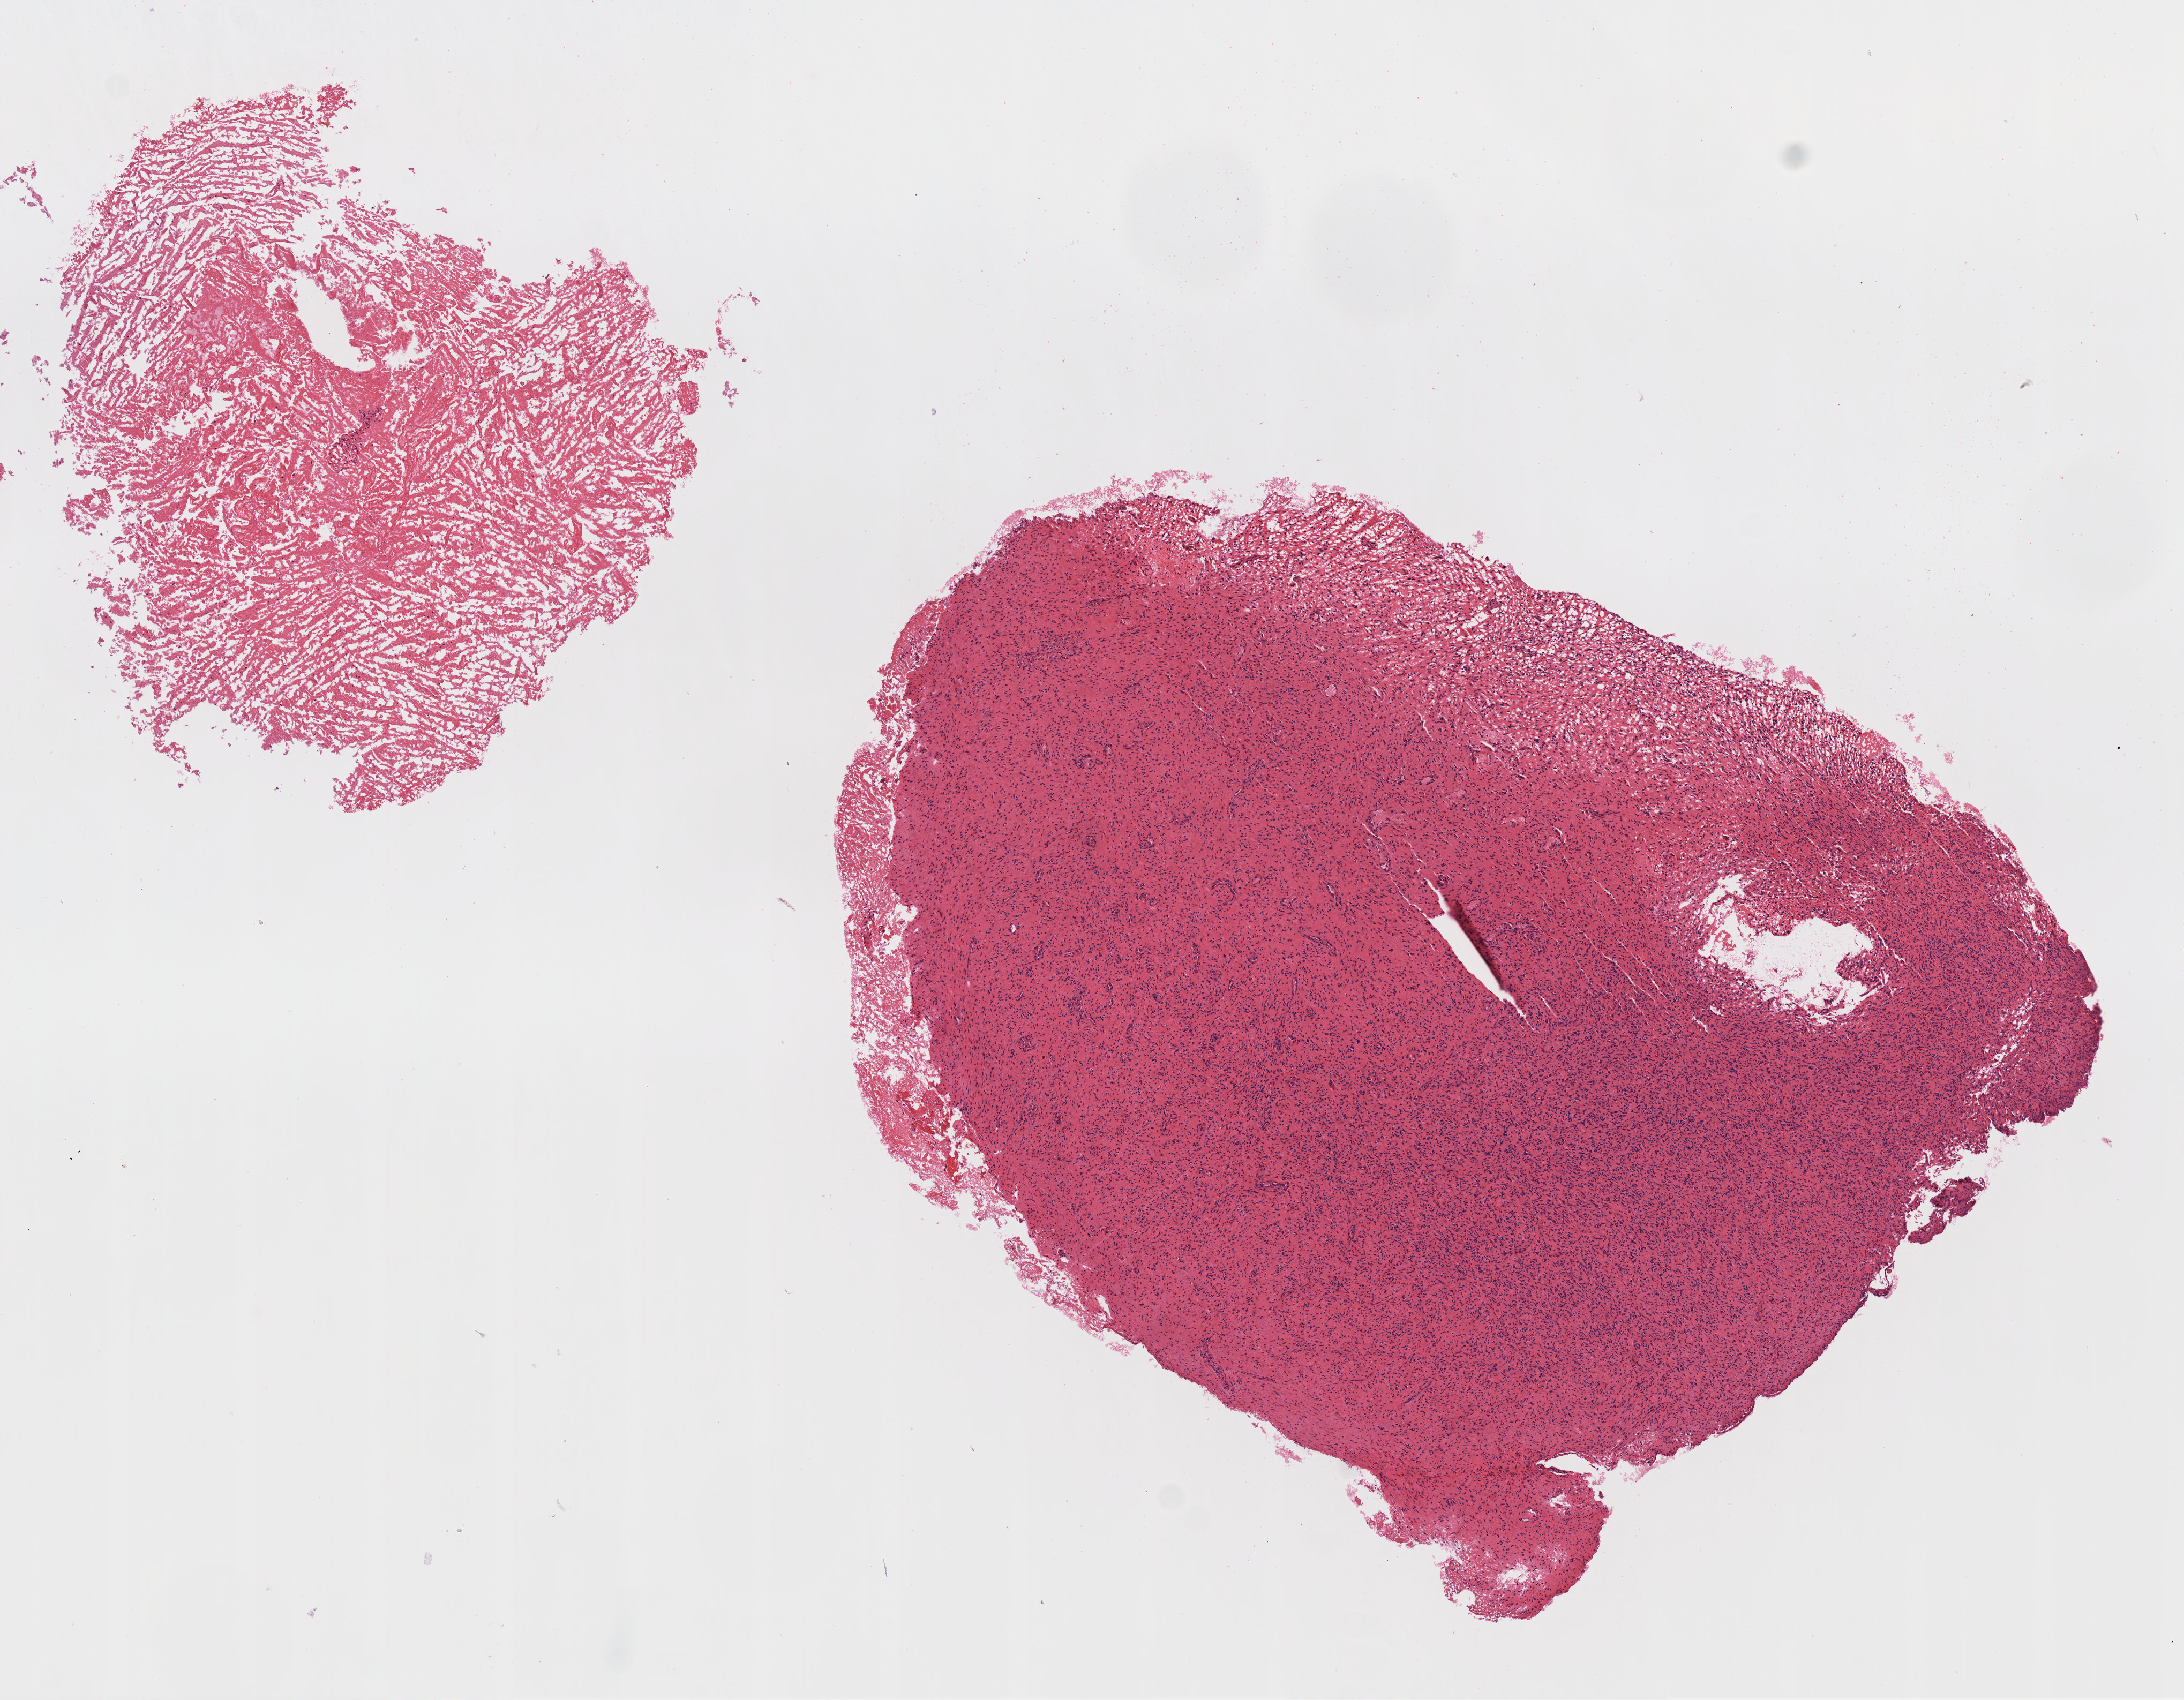
Digitized H&E-stained tissue section (whole slide), low-resolution overview of the scanned area, about 8.2 x 6.4 mm (slide scanned at 20x); formalin-fixed paraffin-embedded (FFPE) diagnostic section; sample: primary tumour, brain. Female patient; age at initial diagnosis 63 years.
Pathologic diagnosis: Glioblastoma.